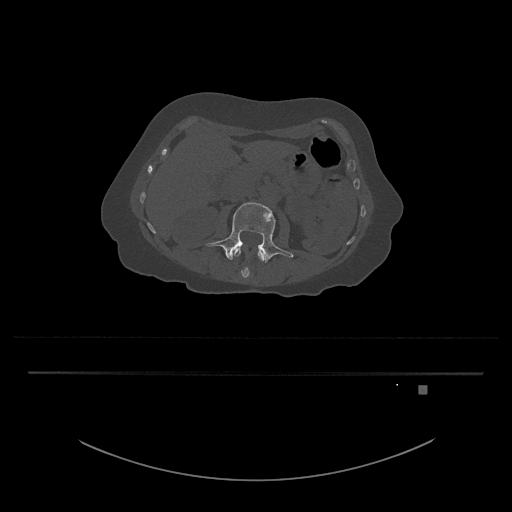
CT including the spine, one axial slice. Slice 443 of 797 in the series (ordered by position). Reconstruction kernel Br40s/3. 120 kVp. Bone window (W 1800 / L 400 HU). 0.5 mm slice thickness. 512 × 512 image matrix, field of view 500 × 500 mm. Patient: female, 57 years. From the clinical record (not read from this slice): primary cancer: cervical.
Outlined on this slice (semi-automatic segmentation, software-assisted and operator-edited):
- L3 vertebra: bounding box <206,202,294,263> (left, top, right, bottom; pixels)